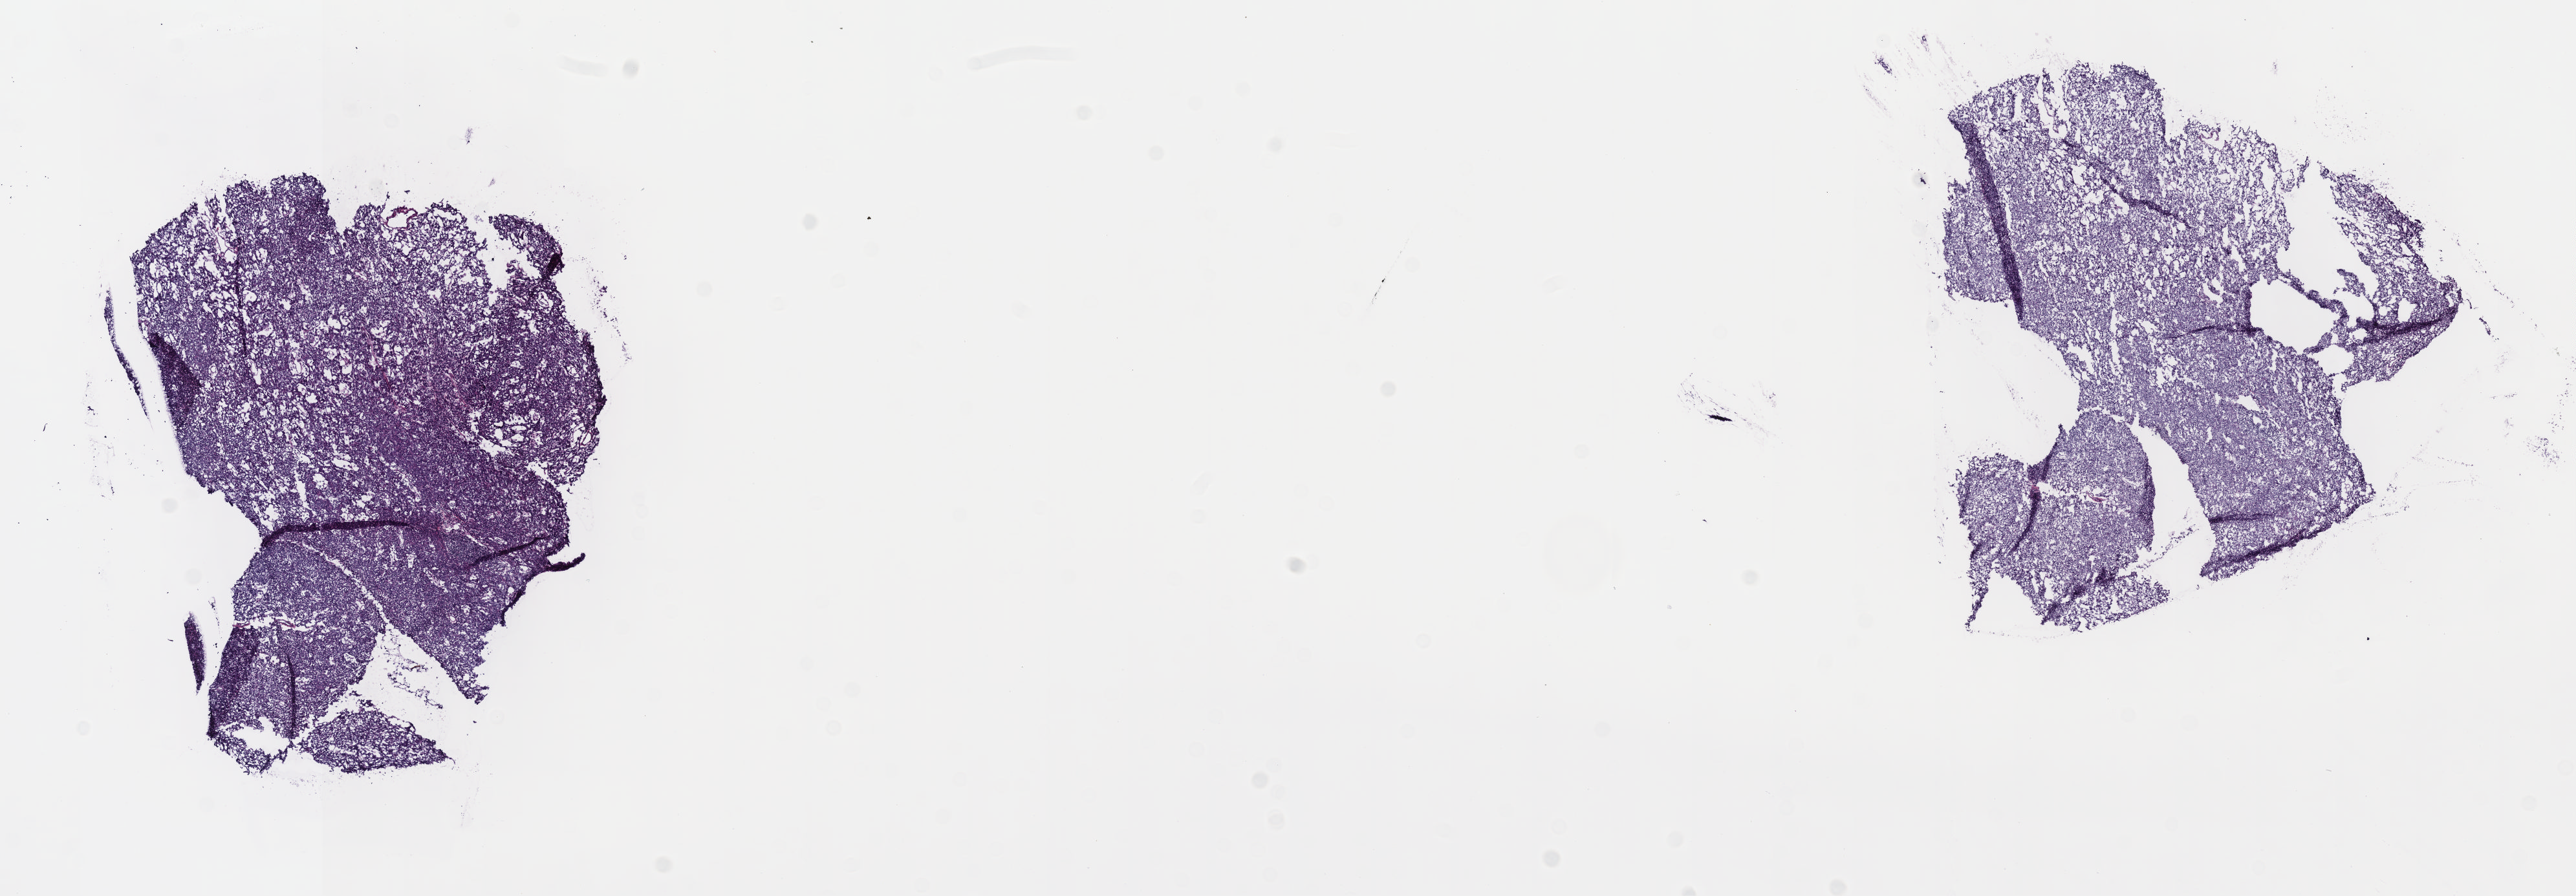
Hematoxylin and eosin (H&E) stained whole-slide image — whole scanned area (about 16.1 x 5.6 mm, slide scanned at 40x) shown as a low-resolution overview. Frozen section. Primary tumour sample from the thymus. Patient: male, age at initial diagnosis 63 years. Pathologist review of this section (percent, as recorded): tumour cells 100%, tumour nuclei 80%, normal cells 0%, stromal cells 0%, necrosis 0%. Infiltration values recorded for this section: lymphocyte infiltration 2%, monocyte infiltration 1%, neutrophil infiltration 0%.
Pathologic diagnosis: Thymoma, type A, NOS.